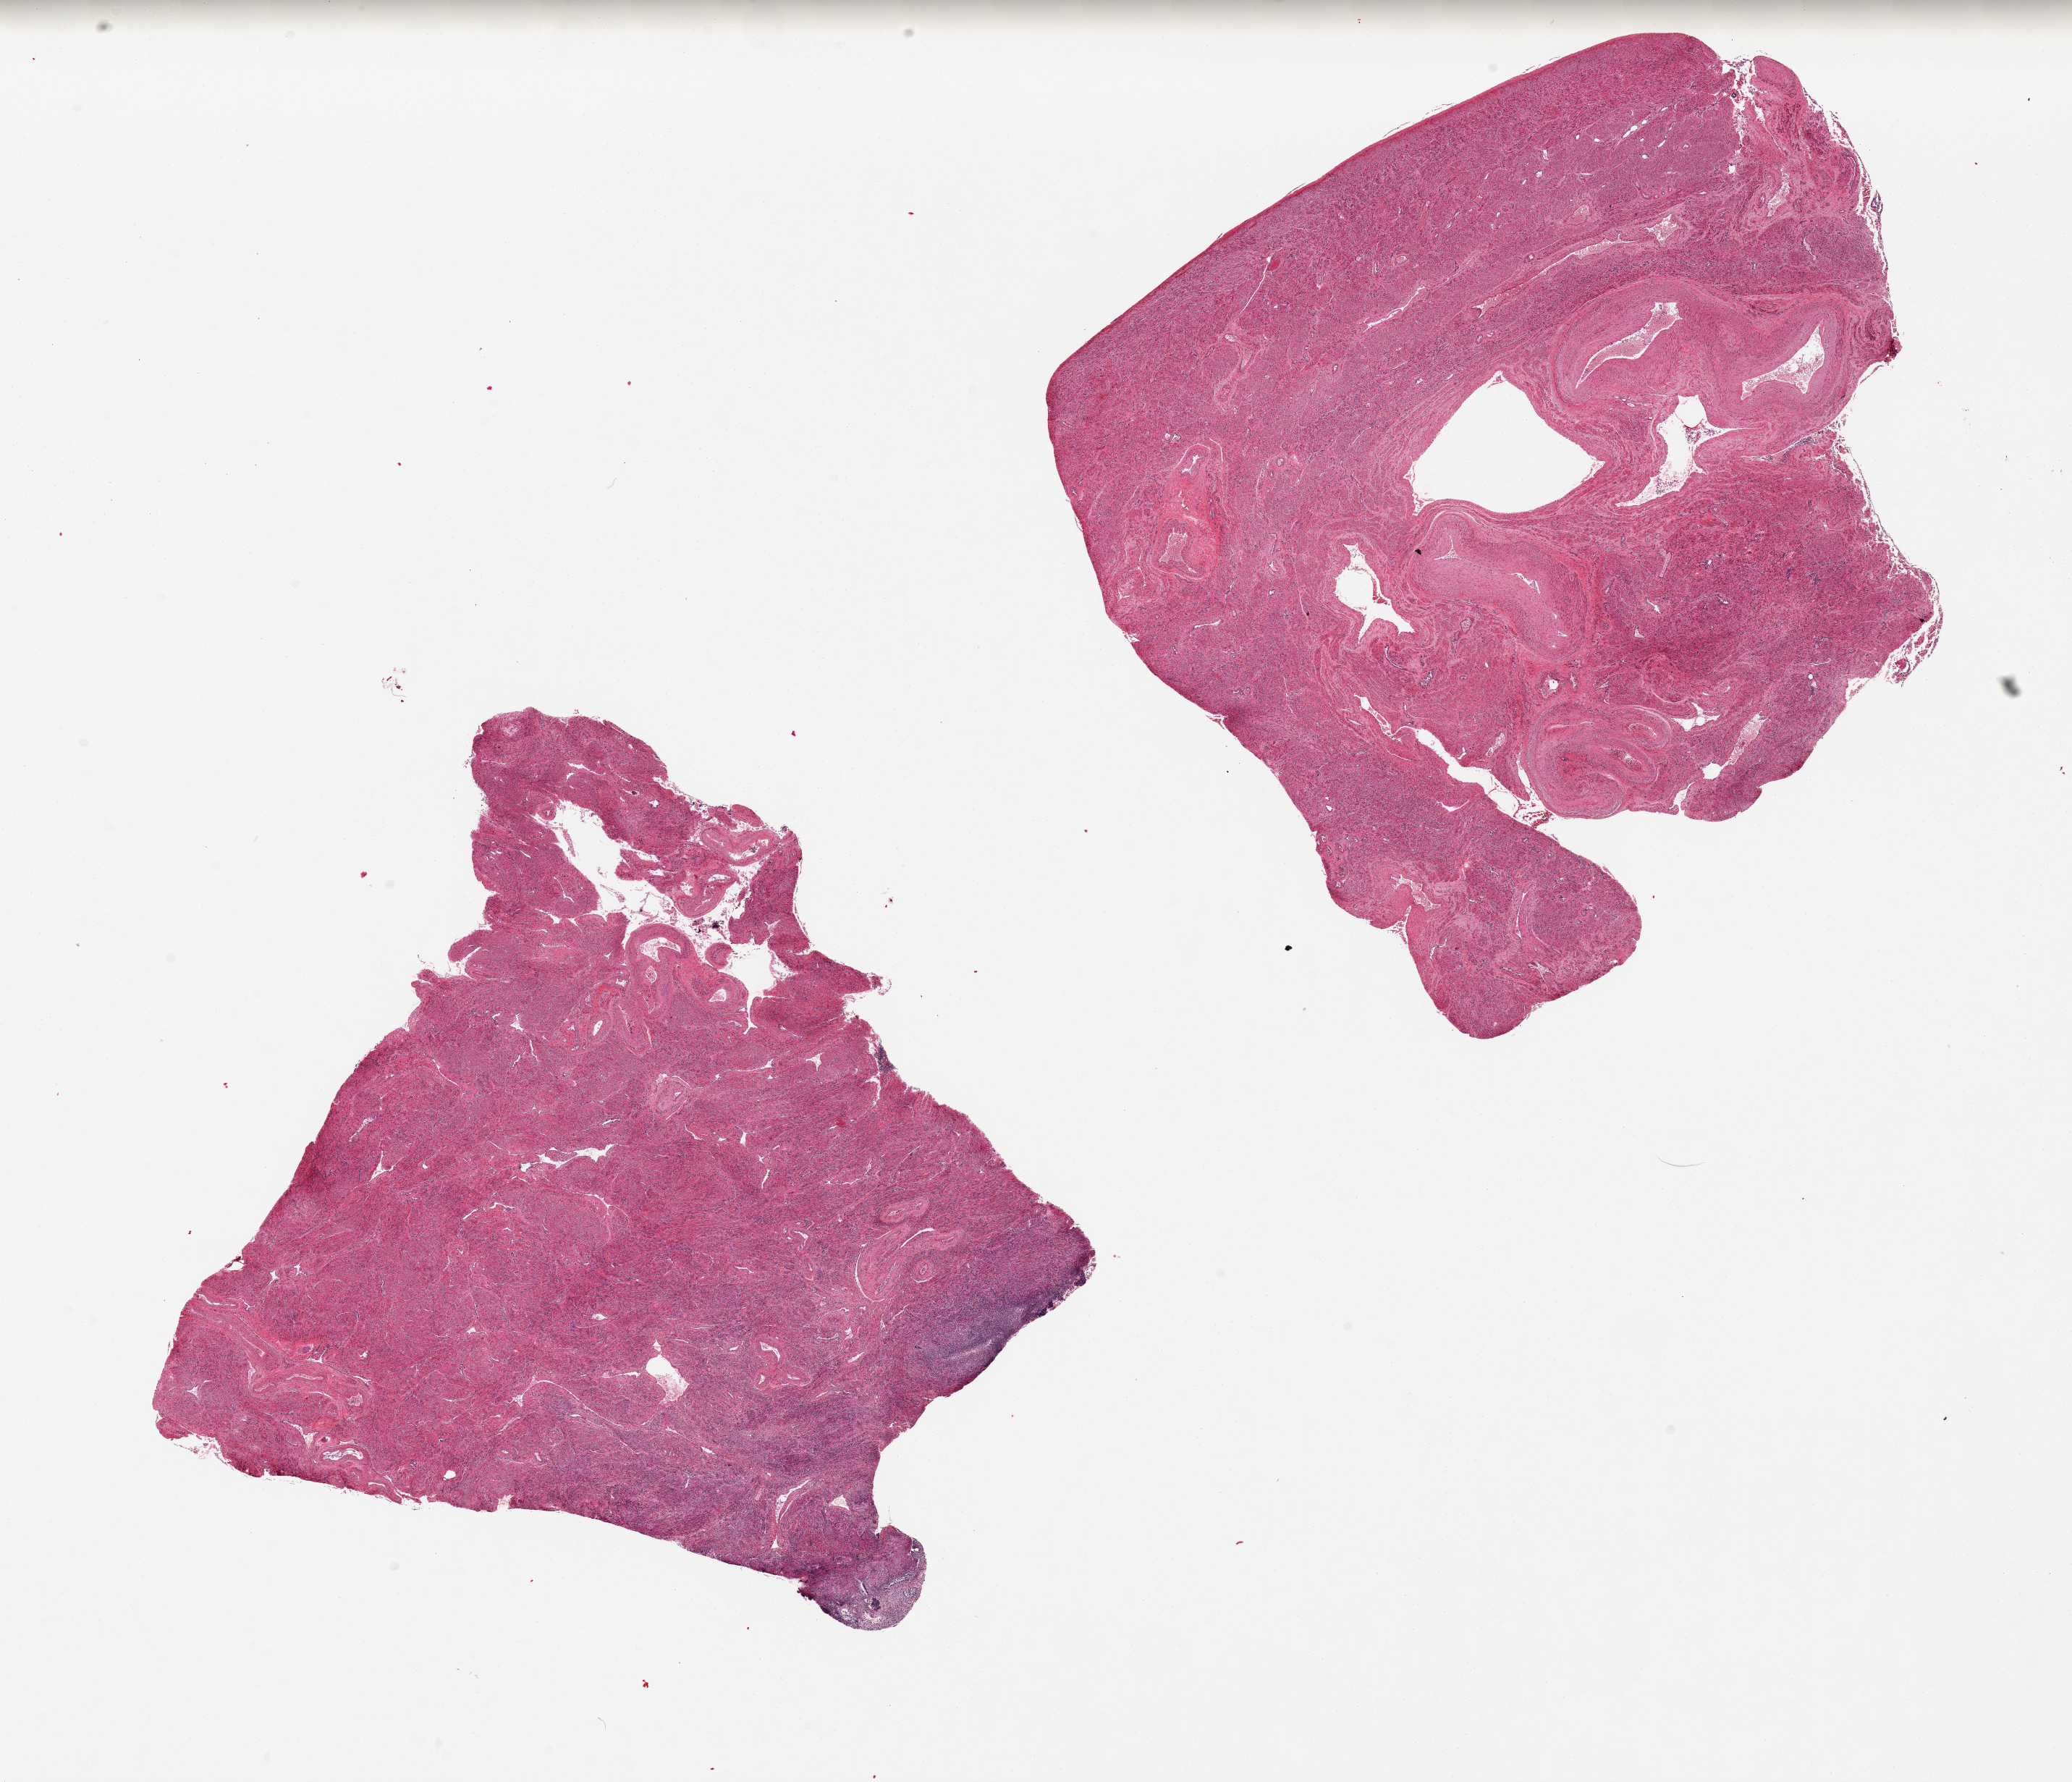
Digitized H&E-stained section, a low-resolution overview of the entire scanned area, about 22.6 x 19.5 mm; PAXgene-fixed paraffin-embedded (PFPE) section; sampled site (target tissue): uterus; tissue donor sample. Female donor.
- review note (as recorded): 2 pieces, 97% myometrium, a few mintue 5mm foci of autolyzed endometrial stroma; no viable glands